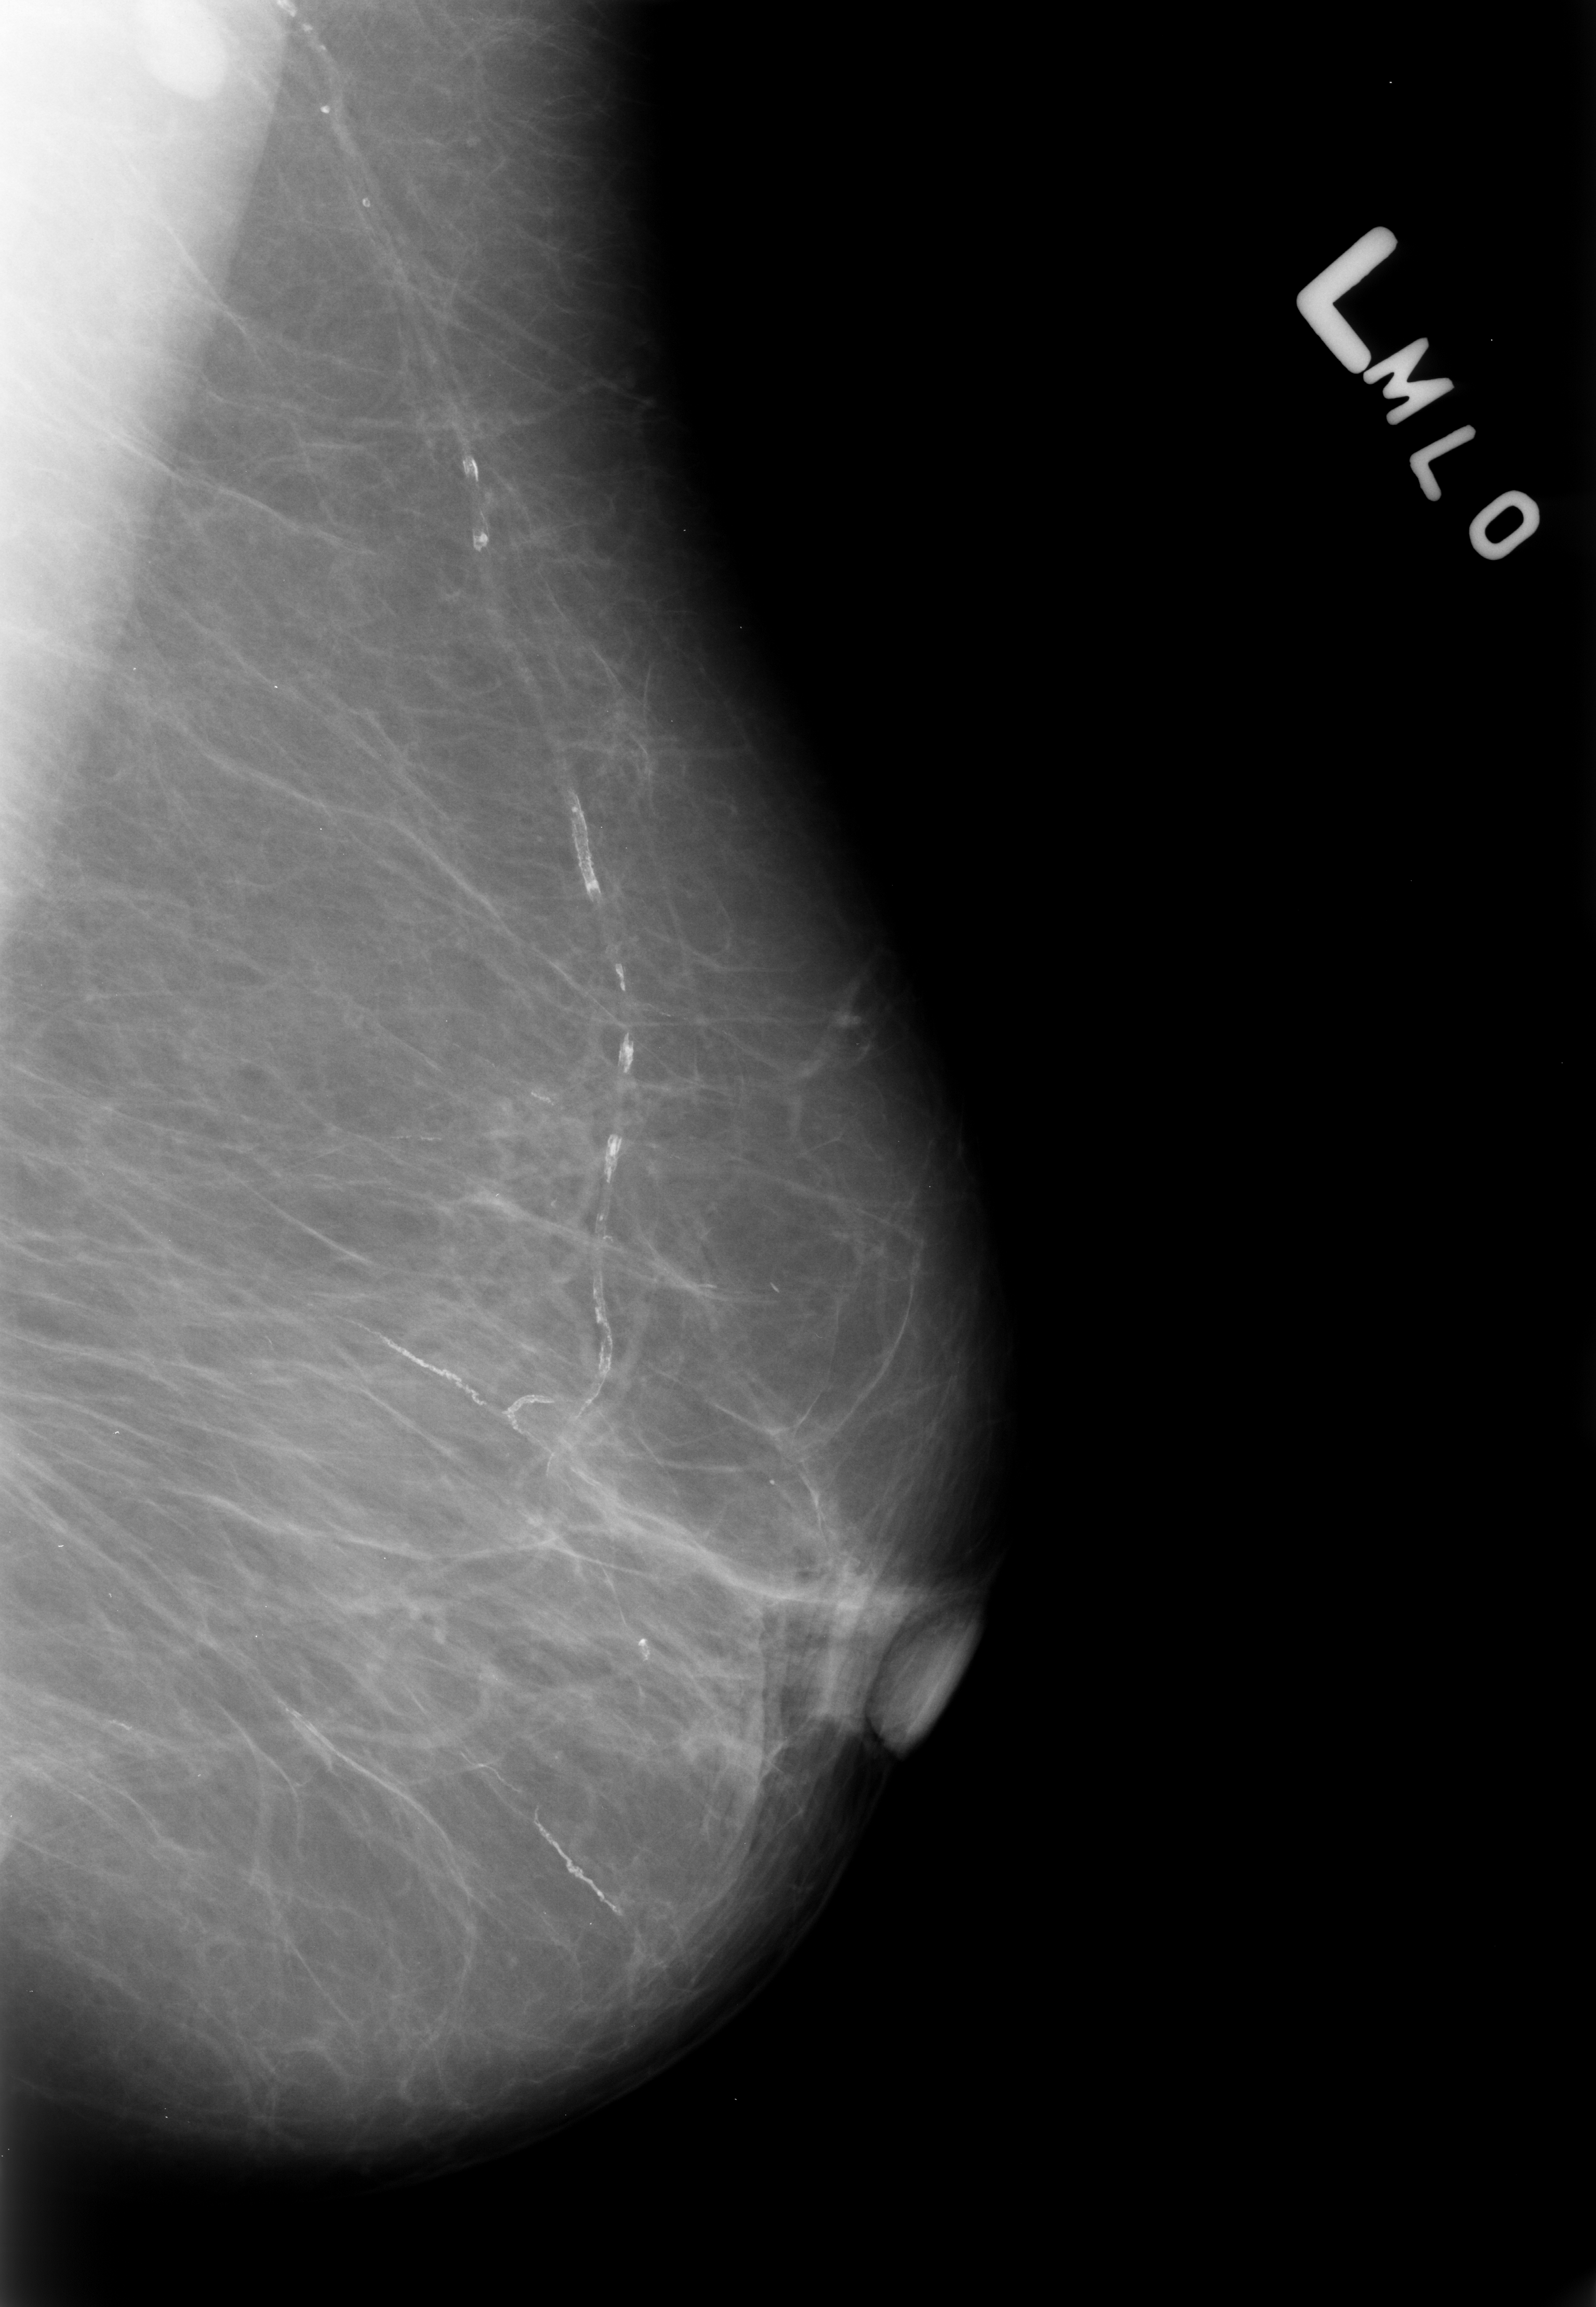
Scanned film-screen mammogram. Left breast. MLO view. BI-RADS breast density category 1 (scale 1–4). 1596 × 2307 image matrix.
Expert-marked regions of interest on this film, with their recorded descriptors:
- Finding 1 of 2: calcifications, morphology vascular; BI-RADS assessment category 2; outcome (as recorded, no biopsy): benign without callback (not worked up further): box from (x=236, y=12) to (x=716, y=1610) px
- Finding 2 of 2: calcifications, morphology vascular; BI-RADS assessment category 2; outcome (as recorded, no biopsy): benign without callback (not worked up further): (x=320, y=1280)–(x=583, y=1435)